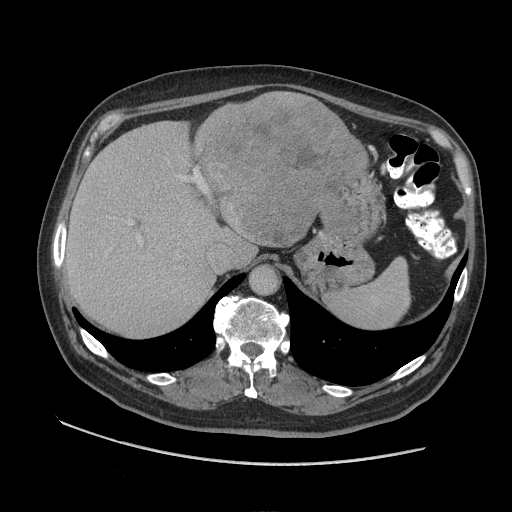
Contrast-enhanced abdominal CT (liver protocol), one axial slice. Slice 69 of 109 in the series (ordered by position). Reconstruction kernel STANDARD. Soft-tissue window (W 400 / L 40 HU). 2.5 mm slice thickness. 512 × 512 image matrix, field of view 420 × 420 mm. From the clinical record (not read from this slice): diagnosis: hepatocellular carcinoma (patient treated with transarterial chemoembolisation; whether this scan precedes or follows treatment is not stated here); TNM stage (as recorded): Stage-I; Child-Pugh class: A; tumour nodularity: uninodular.
Structures marked on this image (semi-automatic segmentation, software-assisted and operator-edited):
- liver parenchyma outside the tumour (the mass and vessels are separate outlines, so this box may not span the whole liver): bounding box (x1, y1, x2, y2) in pixels: (64, 98, 368, 336)
- mass: (197, 91, 367, 247)
- liver vessels: (128, 169, 207, 243)